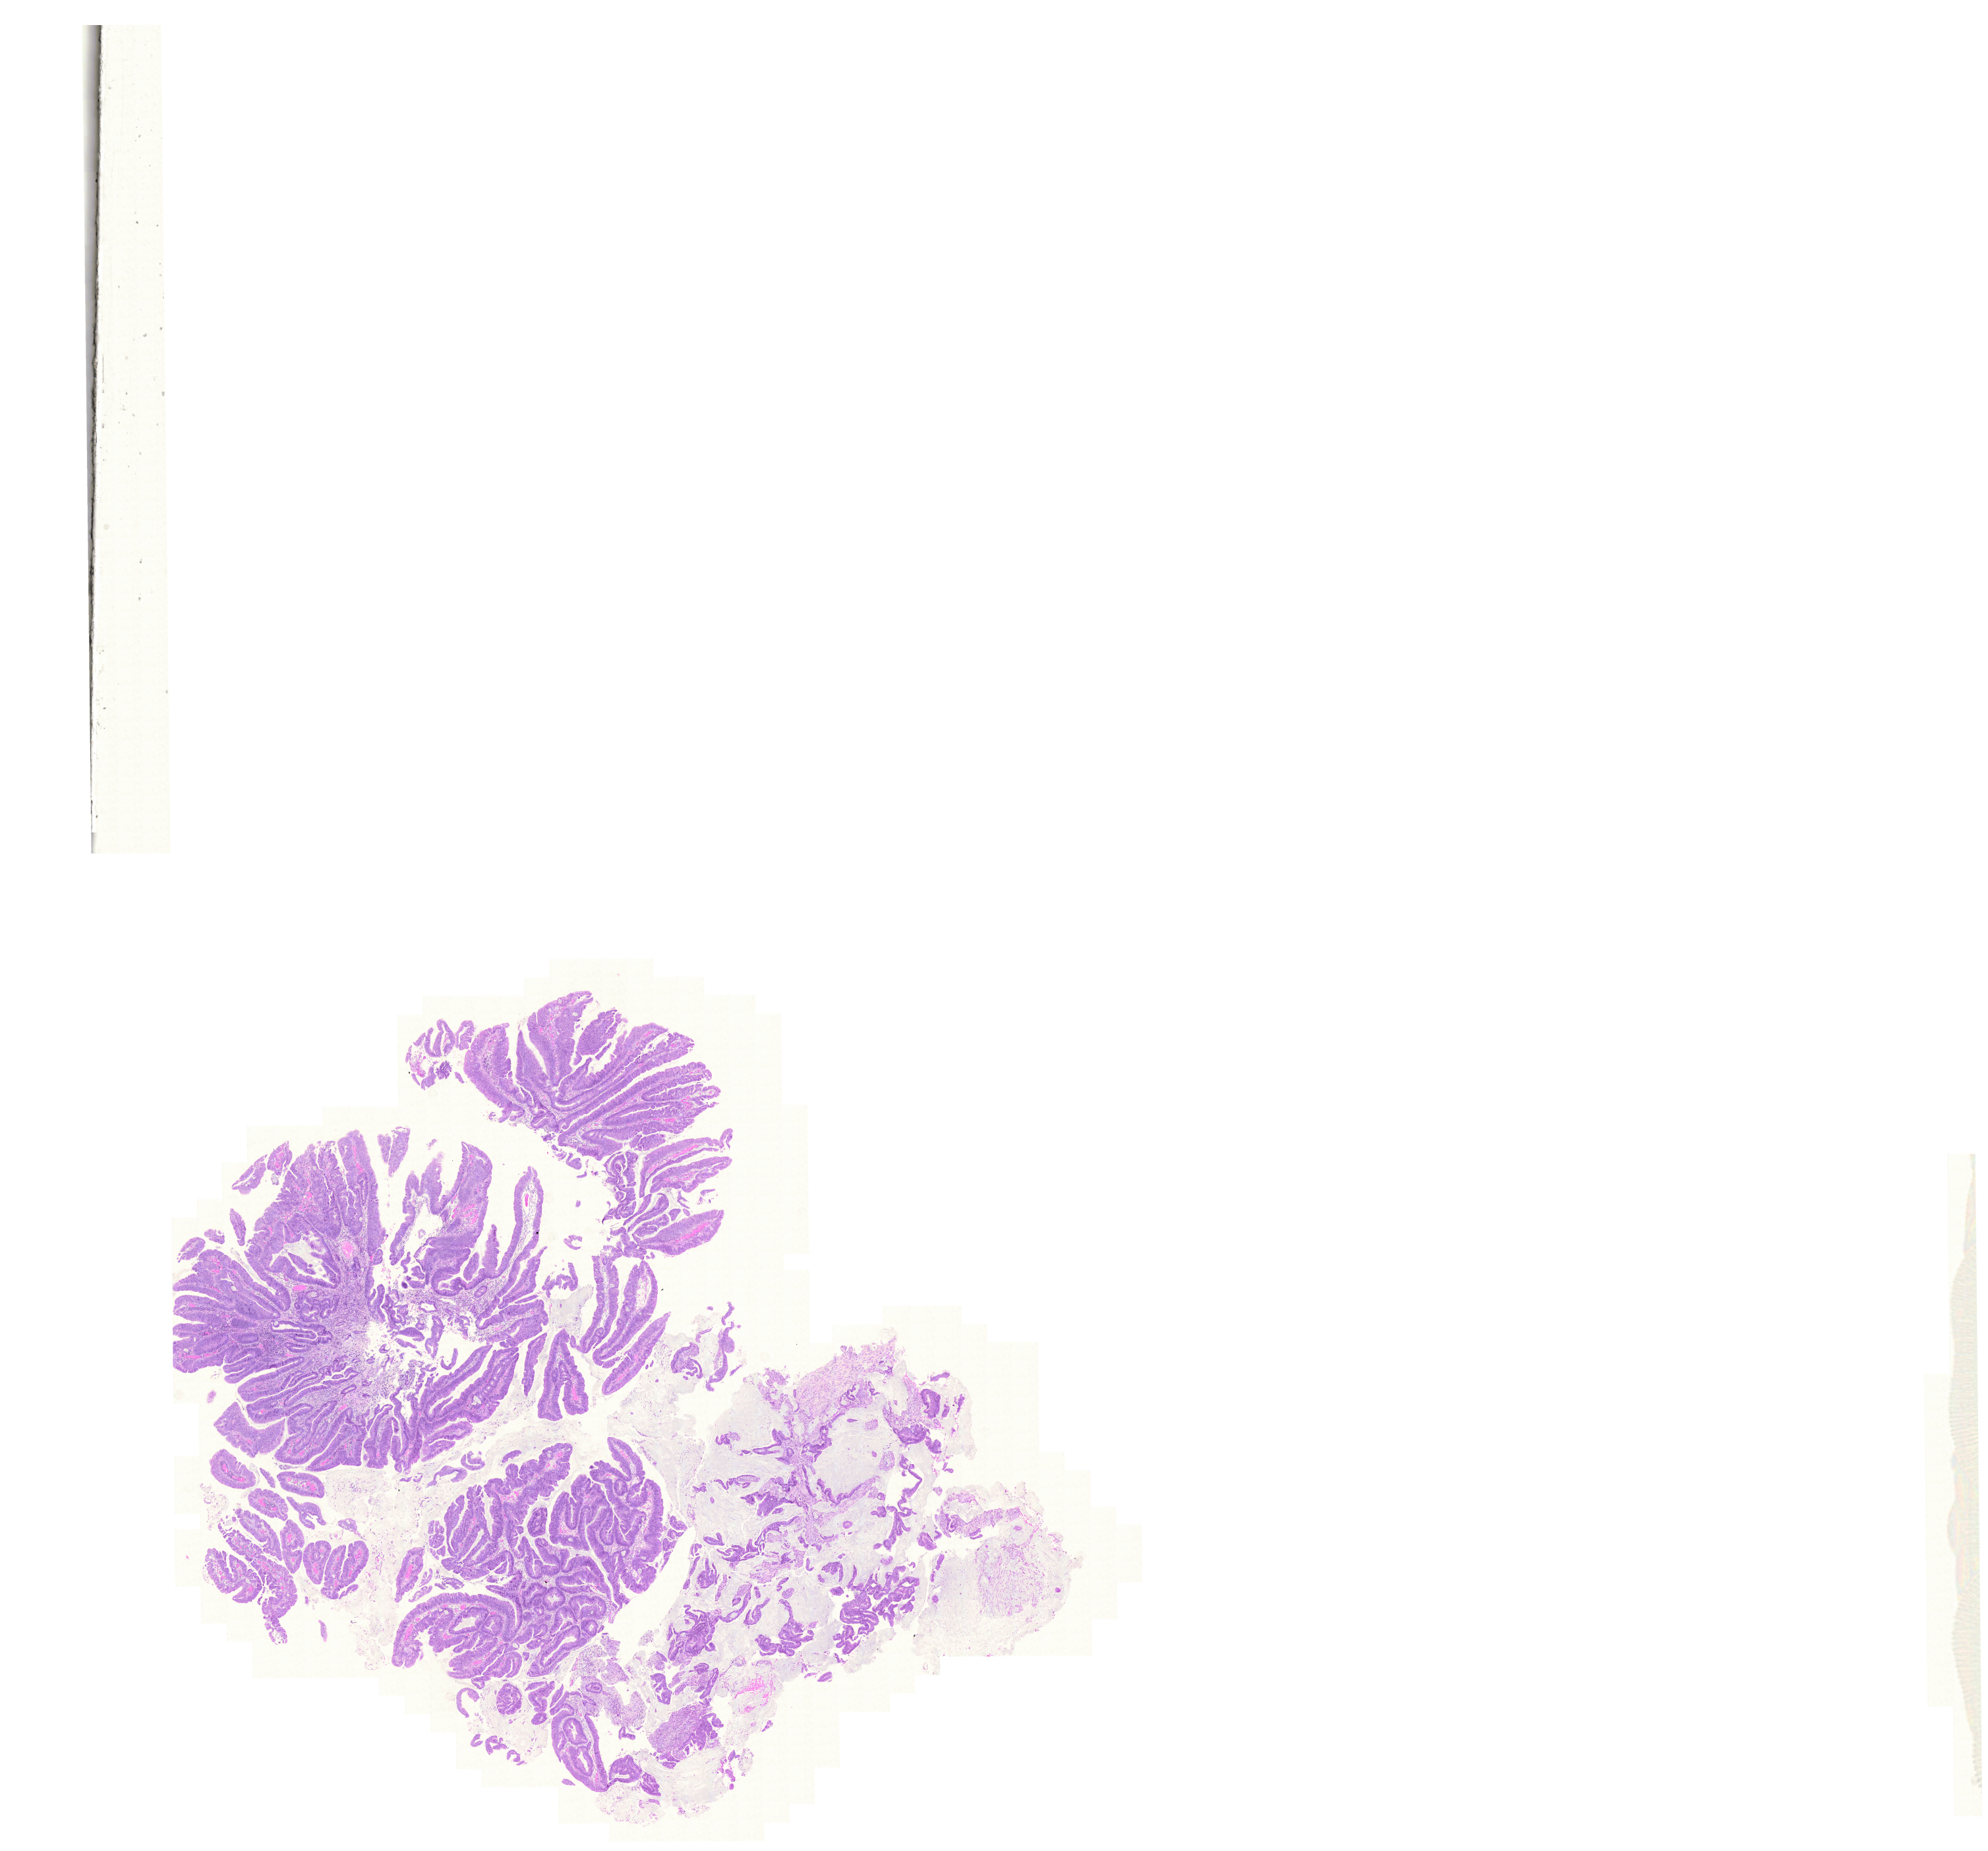
Hematoxylin and eosin (H&E) stained whole-slide image — shown as a low-resolution overview of the whole scanned area (about 22.4 x 20.9 mm), formalin-fixed paraffin-embedded (FFPE) diagnostic section, primary tumour sample from the rectum. Female, age 57 years at initial diagnosis.
• TNM: T3 N1 M0
• lymph nodes positive (case pathology): 1 of 12 examined
• histologic diagnosis: Mucinous adenocarcinoma
• AJCC pathologic stage: III (5th edition)